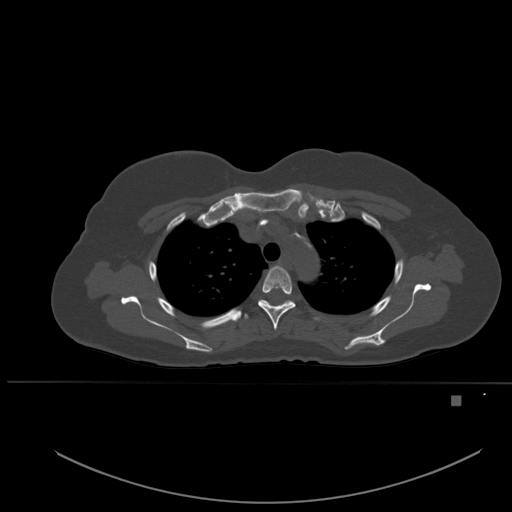
CT including the spine, one axial slice. Slice 391 of 651 in the series (ordered by position). Bone window (W 1800 / L 400 HU). 512 × 512 image matrix, field of view 443 × 443 mm. Female patient, age 49 years. Case-level facts recorded for this patient, not image findings: primary cancer: breast; vertebrae with lytic lesions (as recorded): L3, T12, L4.
Outlined on this slice (semi-automatic segmentation, software-assisted and operator-edited):
- T3 vertebra: bounding box <258,266,295,331> (left, top, right, bottom; pixels)
- T4 vertebra: <244,300,291,319>